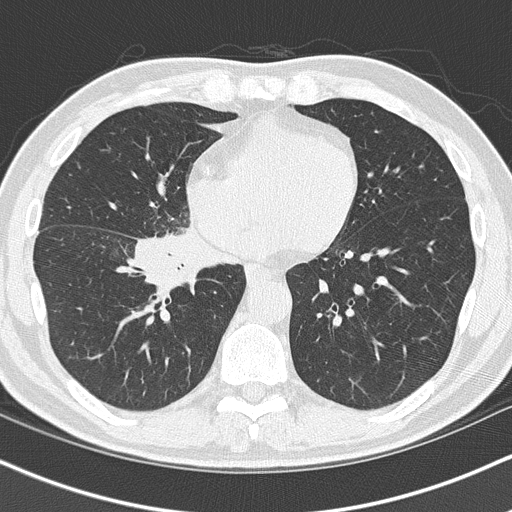
Low-dose screening chest CT, one axial slice. Slice 50 of 151 in the series (ordered by position). 120 kVp. Lung window (W 1500 / L -600 HU). 2 mm slice thickness. 512 × 512 image matrix.
Annotated regions visible in this slice (expert manual segmentation):
- lesion 1 (tumor, hilum of right lung): box from (x=136, y=234) to (x=202, y=286) px